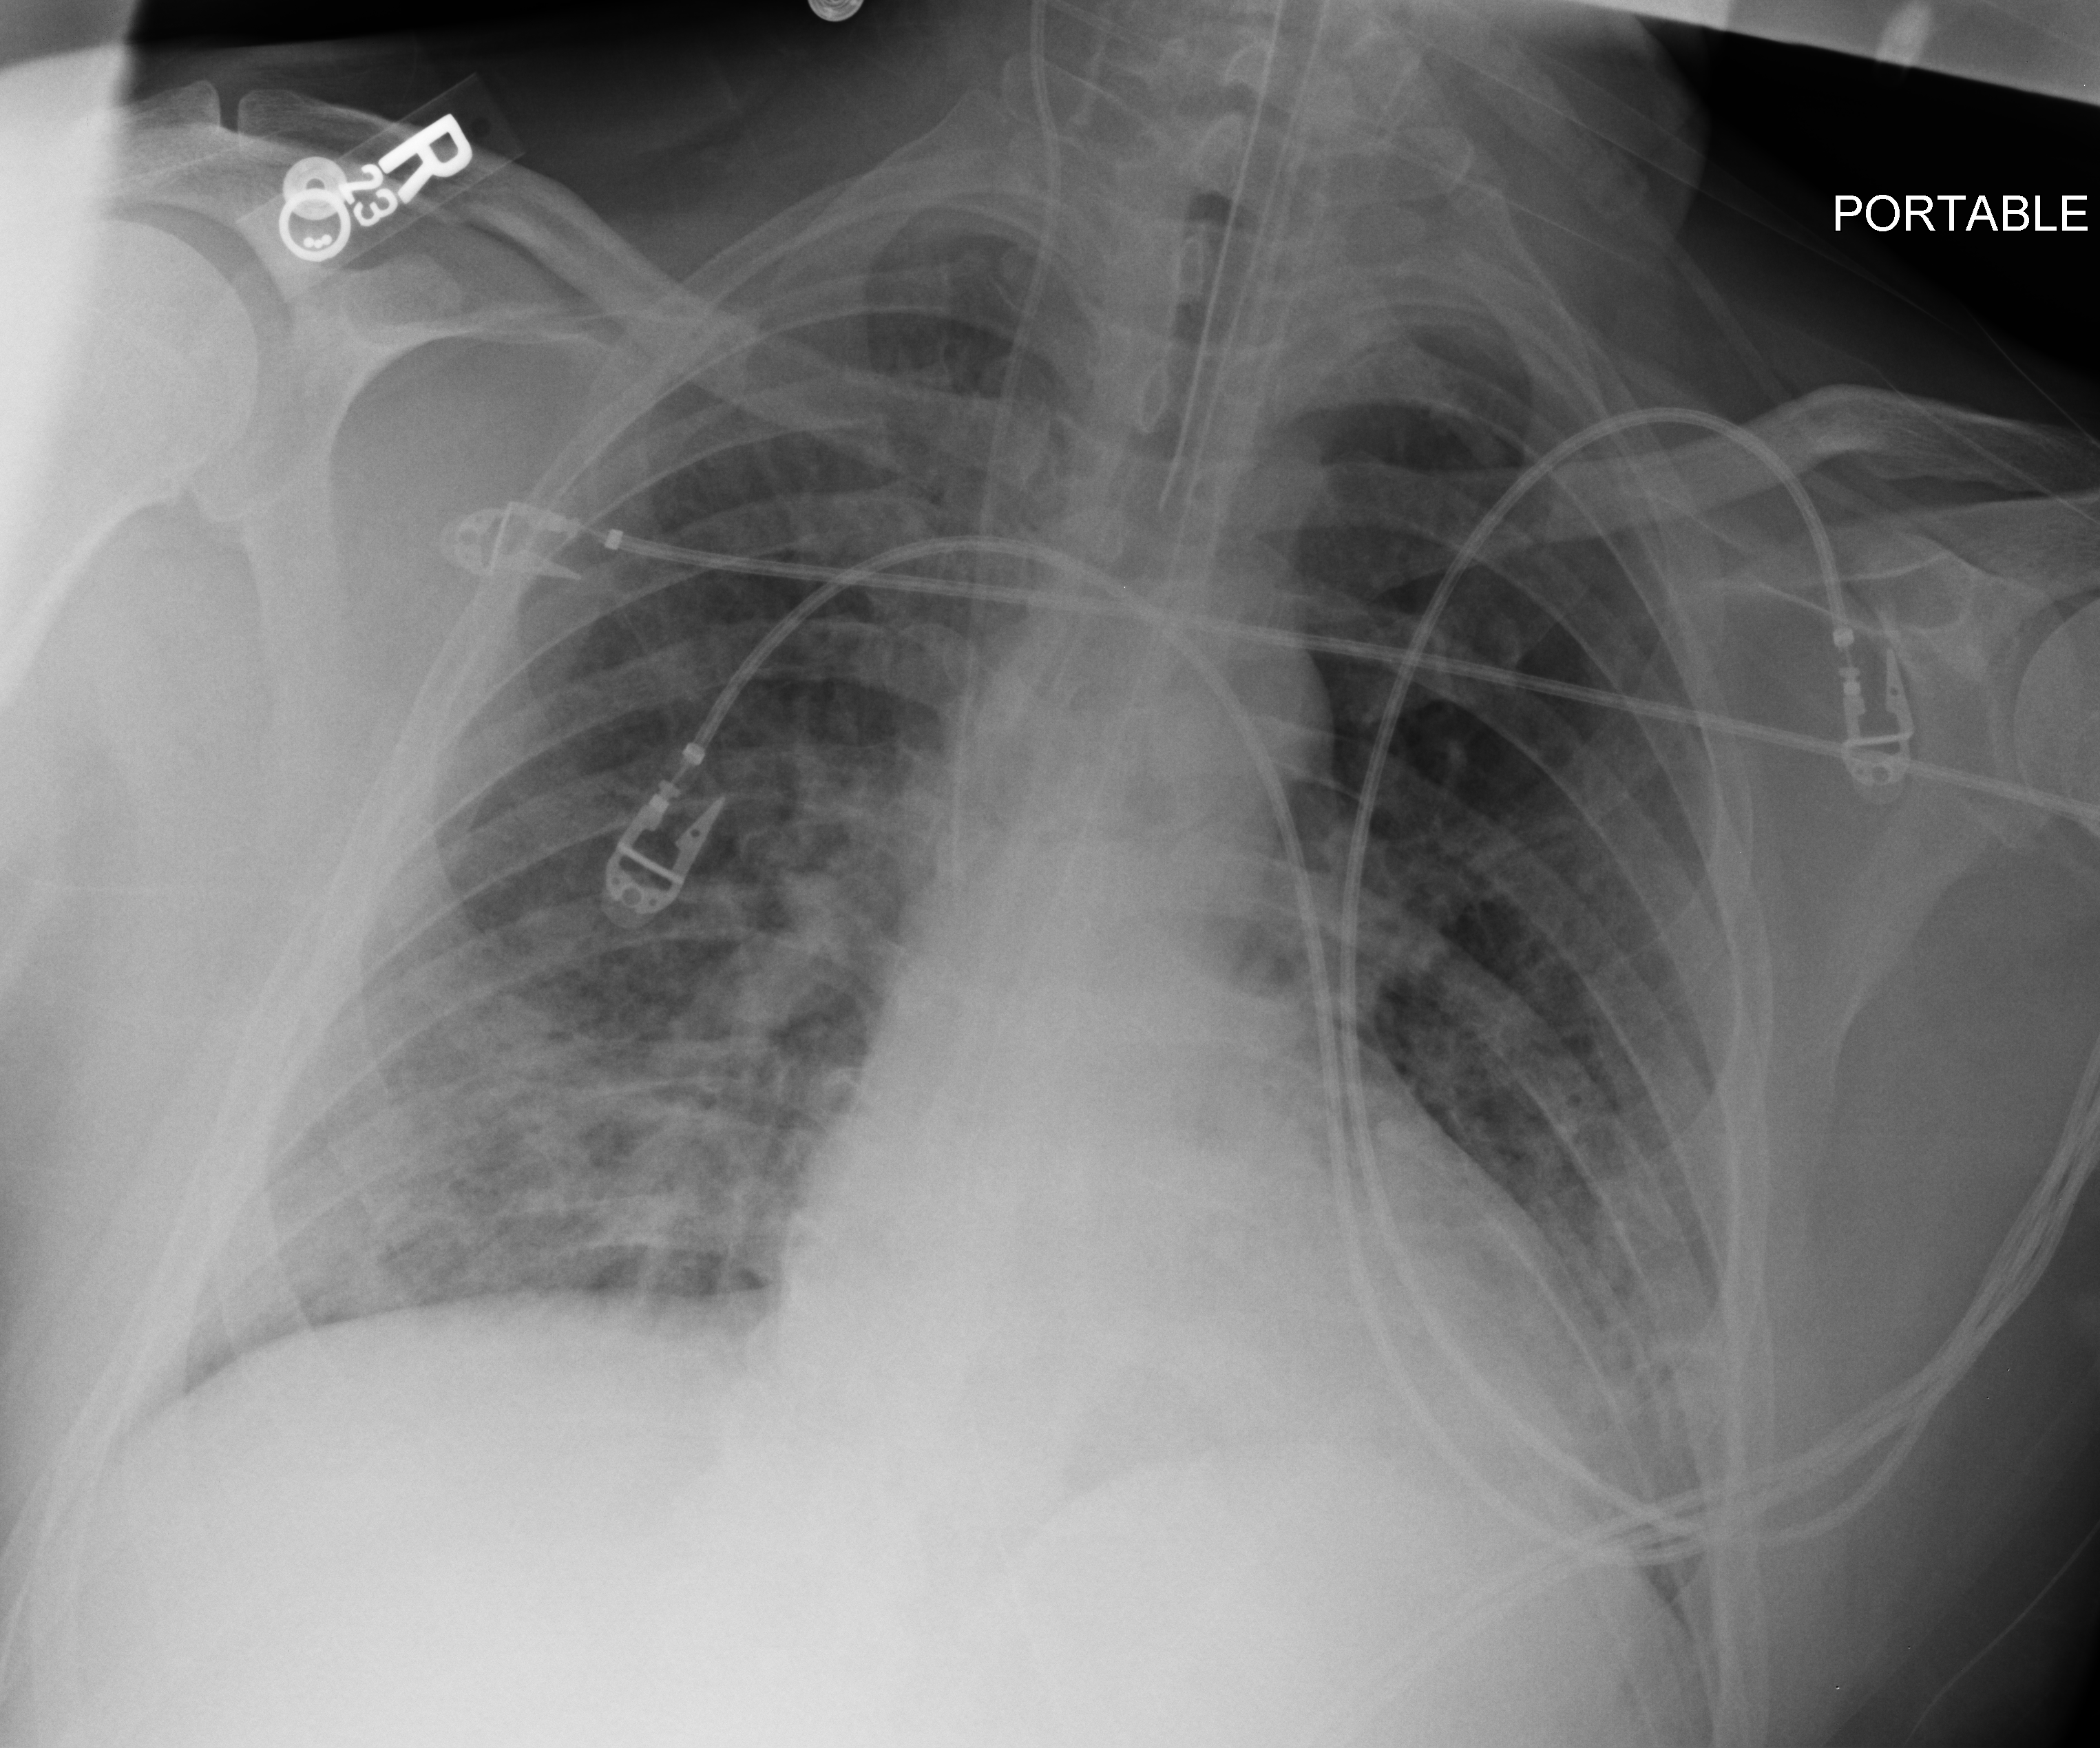
Bedside chest radiograph (computed radiography); anteroposterior (AP) projection. Male patient hospitalised with COVID-19, age 18–59 years.
Admission-level facts for this patient (not findings on this image; timing relative to this image not recorded):
- admitted to intensive care during this hospital stay: no
- mechanically ventilated during this hospital stay: yes